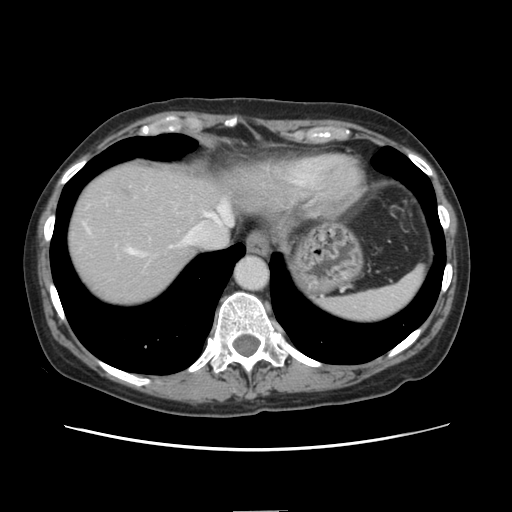
Contrast-enhanced abdominal CT, one axial slice. Position 122 of 141 along the scan axis. Soft-tissue window (W 400 / L 40 HU). 2.5 mm slice thickness. 512 × 512 image matrix, field of view 350 × 350 mm. Female patient, age 63 years. From the clinical record (not read from this slice): diagnosis: colorectal cancer liver metastases, imaged before liver resection; multiple liver metastases: yes; largest metastasis: 3.2 cm.
Structures marked on this image (manually delineated by an expert):
- hepatic veins: bounding box (x1, y1, x2, y2) in pixels: (127, 204, 230, 254)
- liver: (67, 161, 297, 308)
- planned liver remnant (the part of the liver to remain after resection): (207, 178, 243, 227)